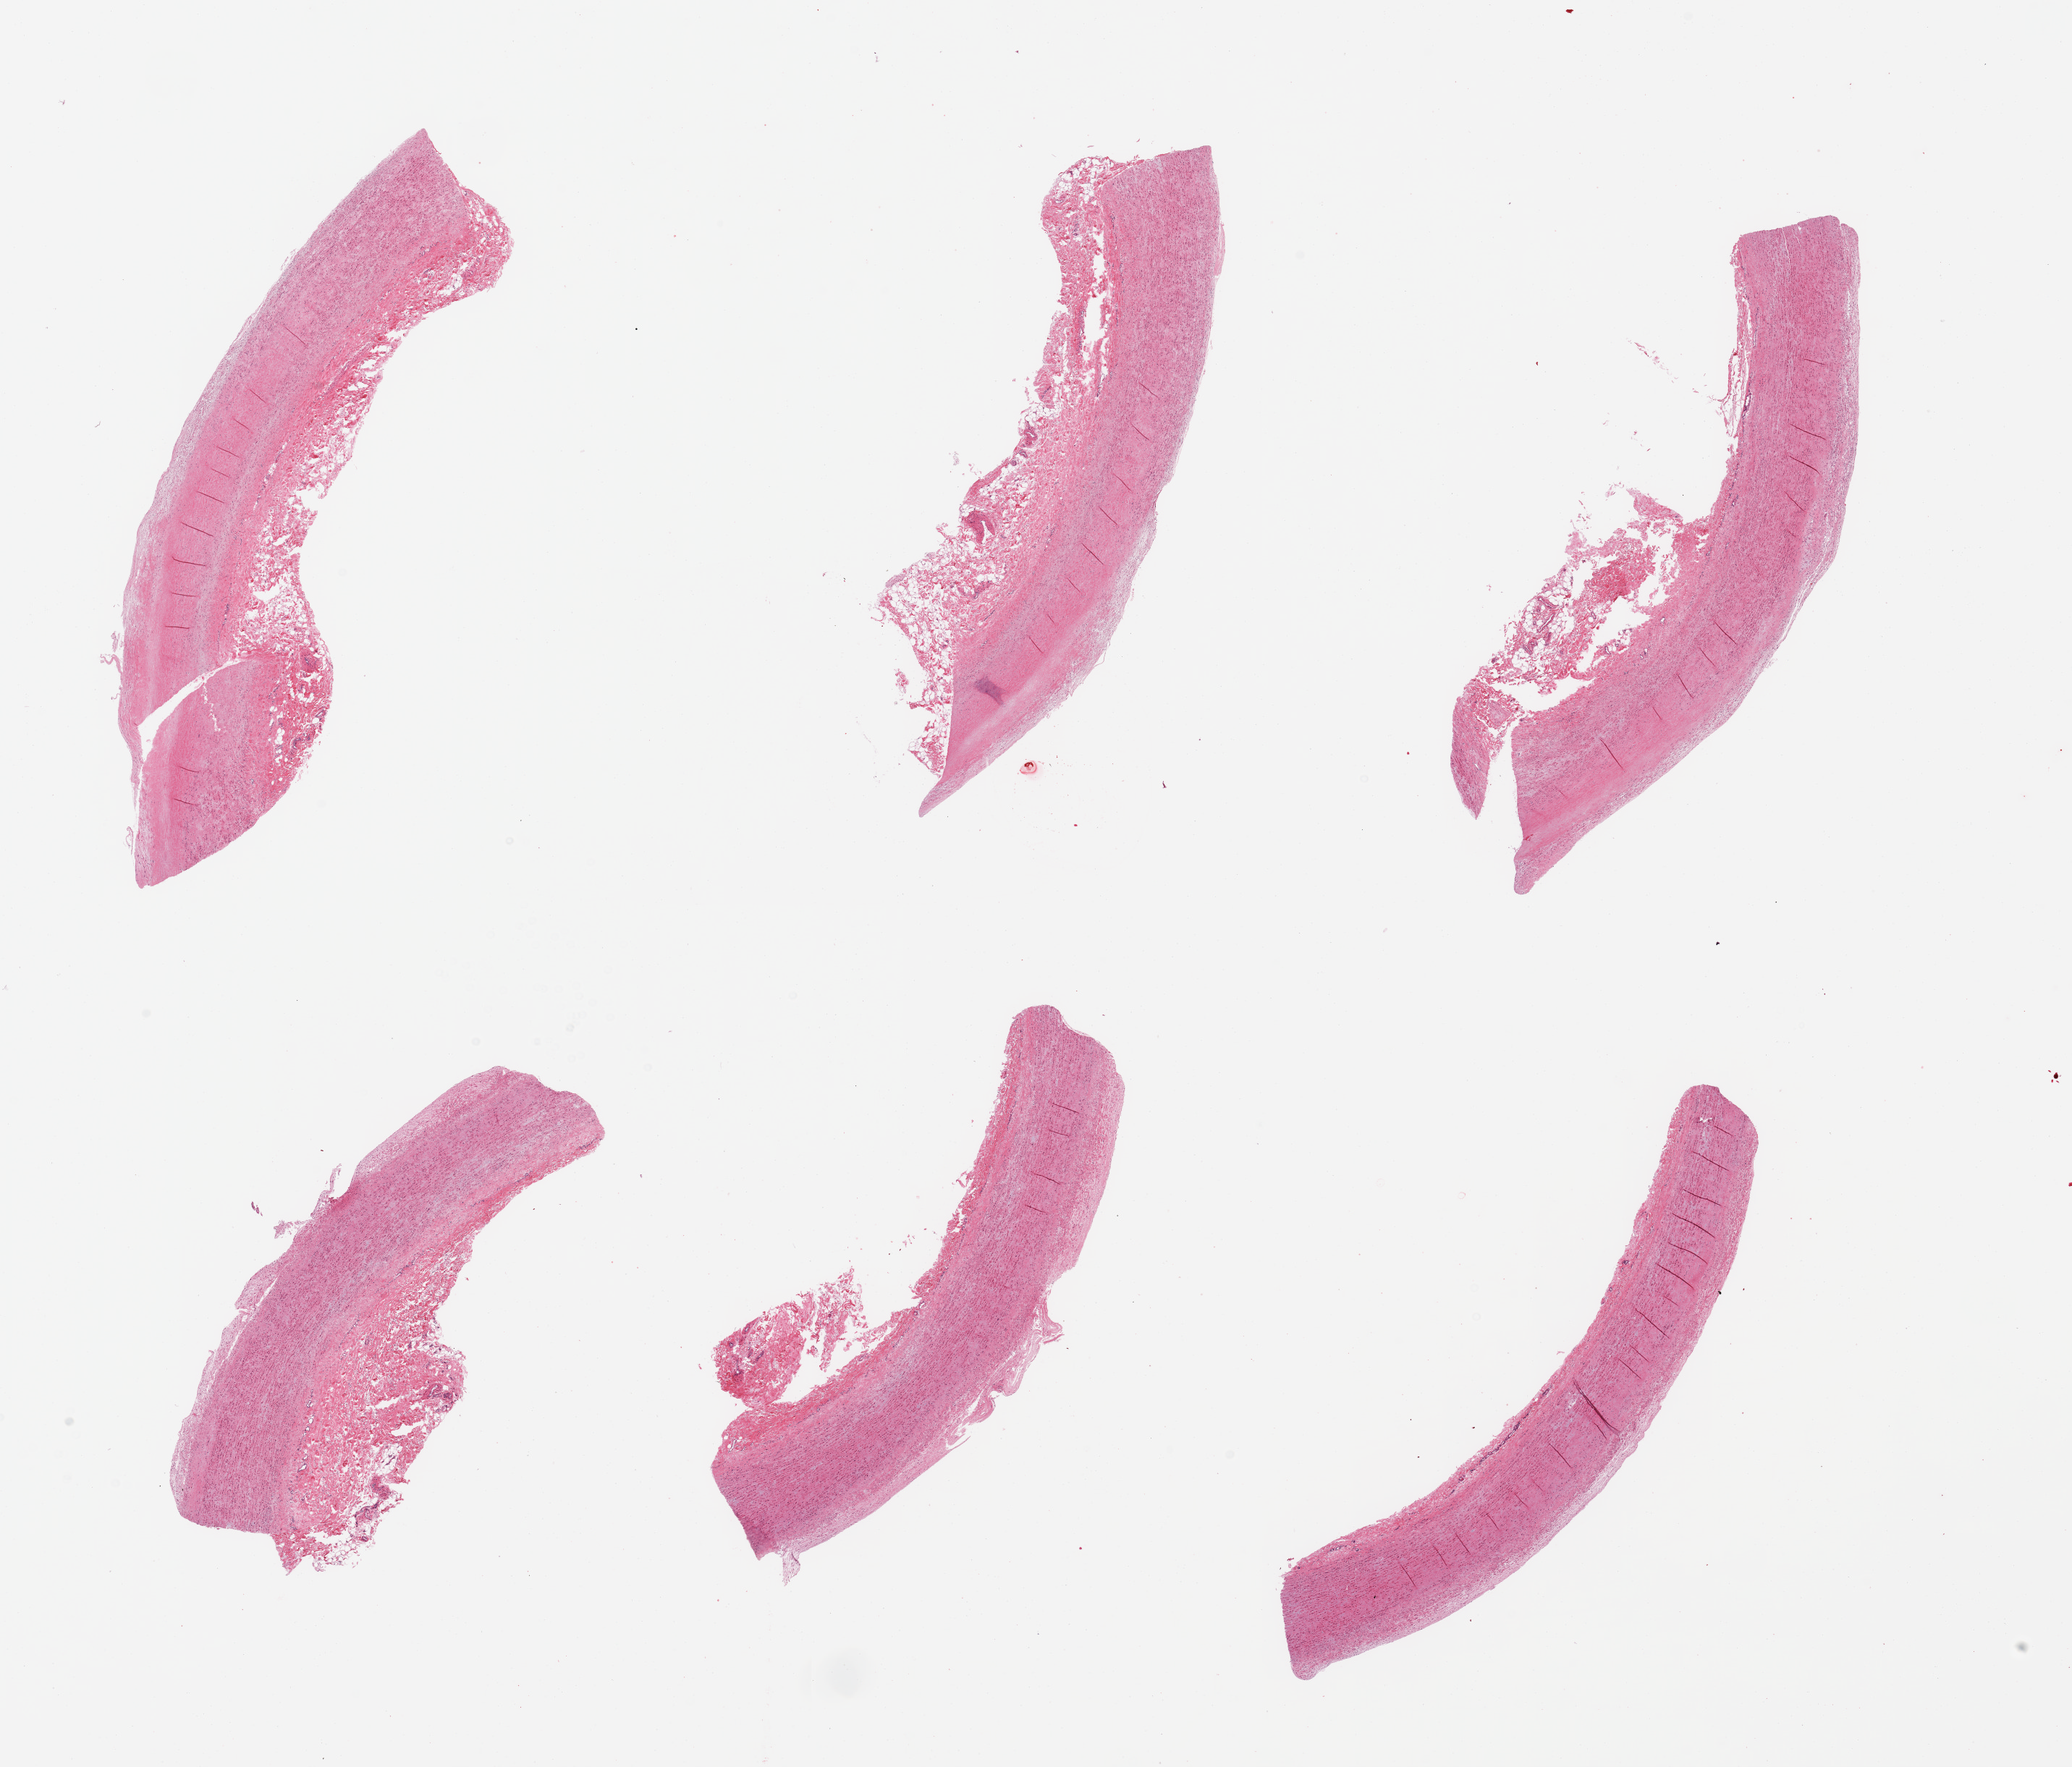
Digitized hematoxylin and eosin (H&E)-stained section — a low-resolution overview of the entire scanned area, about 22.6 x 19.3 mm (acquisition: 20x scan). PAXgene-fixed, paraffin-embedded tissue. Section of aorta (target tissue). Donor tissue sample. Donor: male.
• reviewer comment on this tissue sample: 6 pieces; atherosclerosis with loss of medial elastic tissue